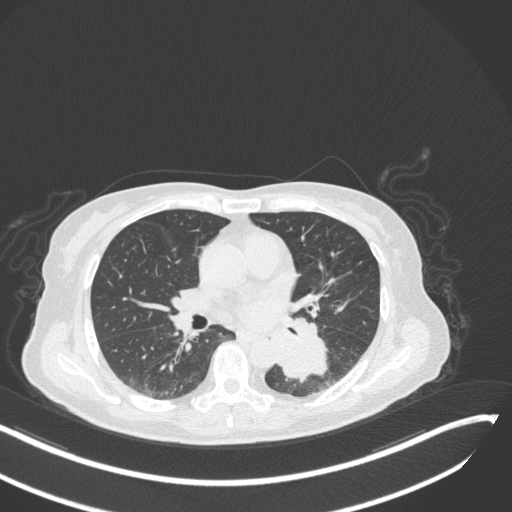
Chest CT, one axial slice; position 142 of 342 along the scan axis; reconstruction kernel B31f; lung window (W 1500 / L -600 HU); 1 mm slice thickness; 512 × 512 image matrix, field of view 400 × 400 mm. Patient: female, 64 years. Case-level facts recorded for this patient, not image findings: clinical TNM (as recorded): T3 N1 M1; histopathological grade: G3.
Annotated regions visible in this slice (rectangle marked by the reading radiologist):
- lung tumour (recorded histology: small cell carcinoma): box from (x=282, y=336) to (x=334, y=386) px